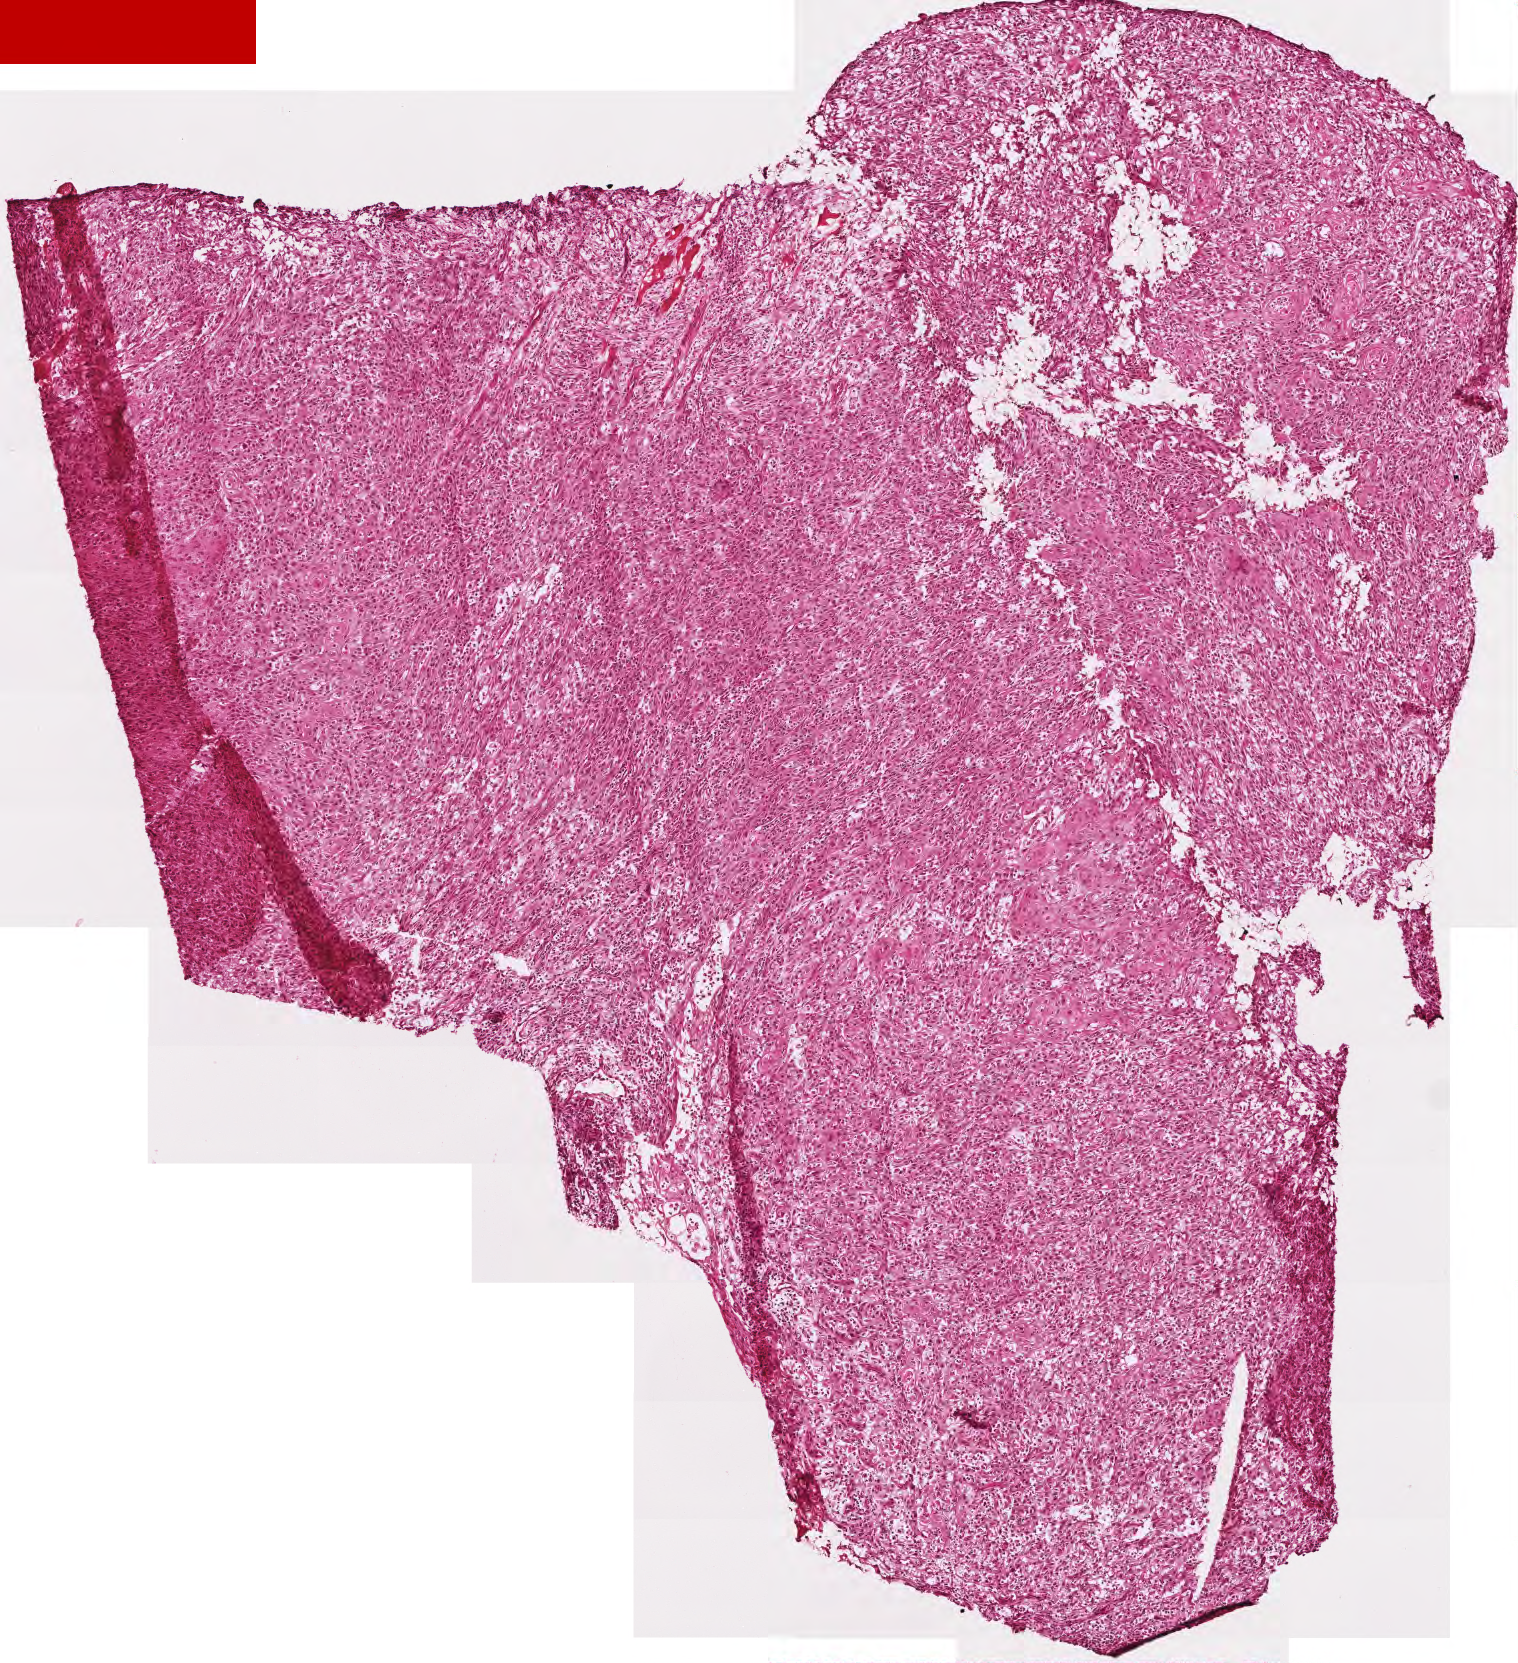
Whole-slide histology image, H&E, low-resolution overview of the scanned area, about 3.0 x 3.3 mm, frozen section from the top of the tissue portion, primary tumour sample from the head and neck. Male, age 49 years at initial diagnosis. Histologic grade: G2 (moderately differentiated). Composition of this section per pathologist review: tumour cells 95%, tumour nuclei 85%, normal cells 0%, stromal cells 5%, necrosis 0%.
AJCC pathologic stage: IVA (6th edition). Histologic diagnosis: Squamous cell carcinoma, NOS (tongue, NOS).